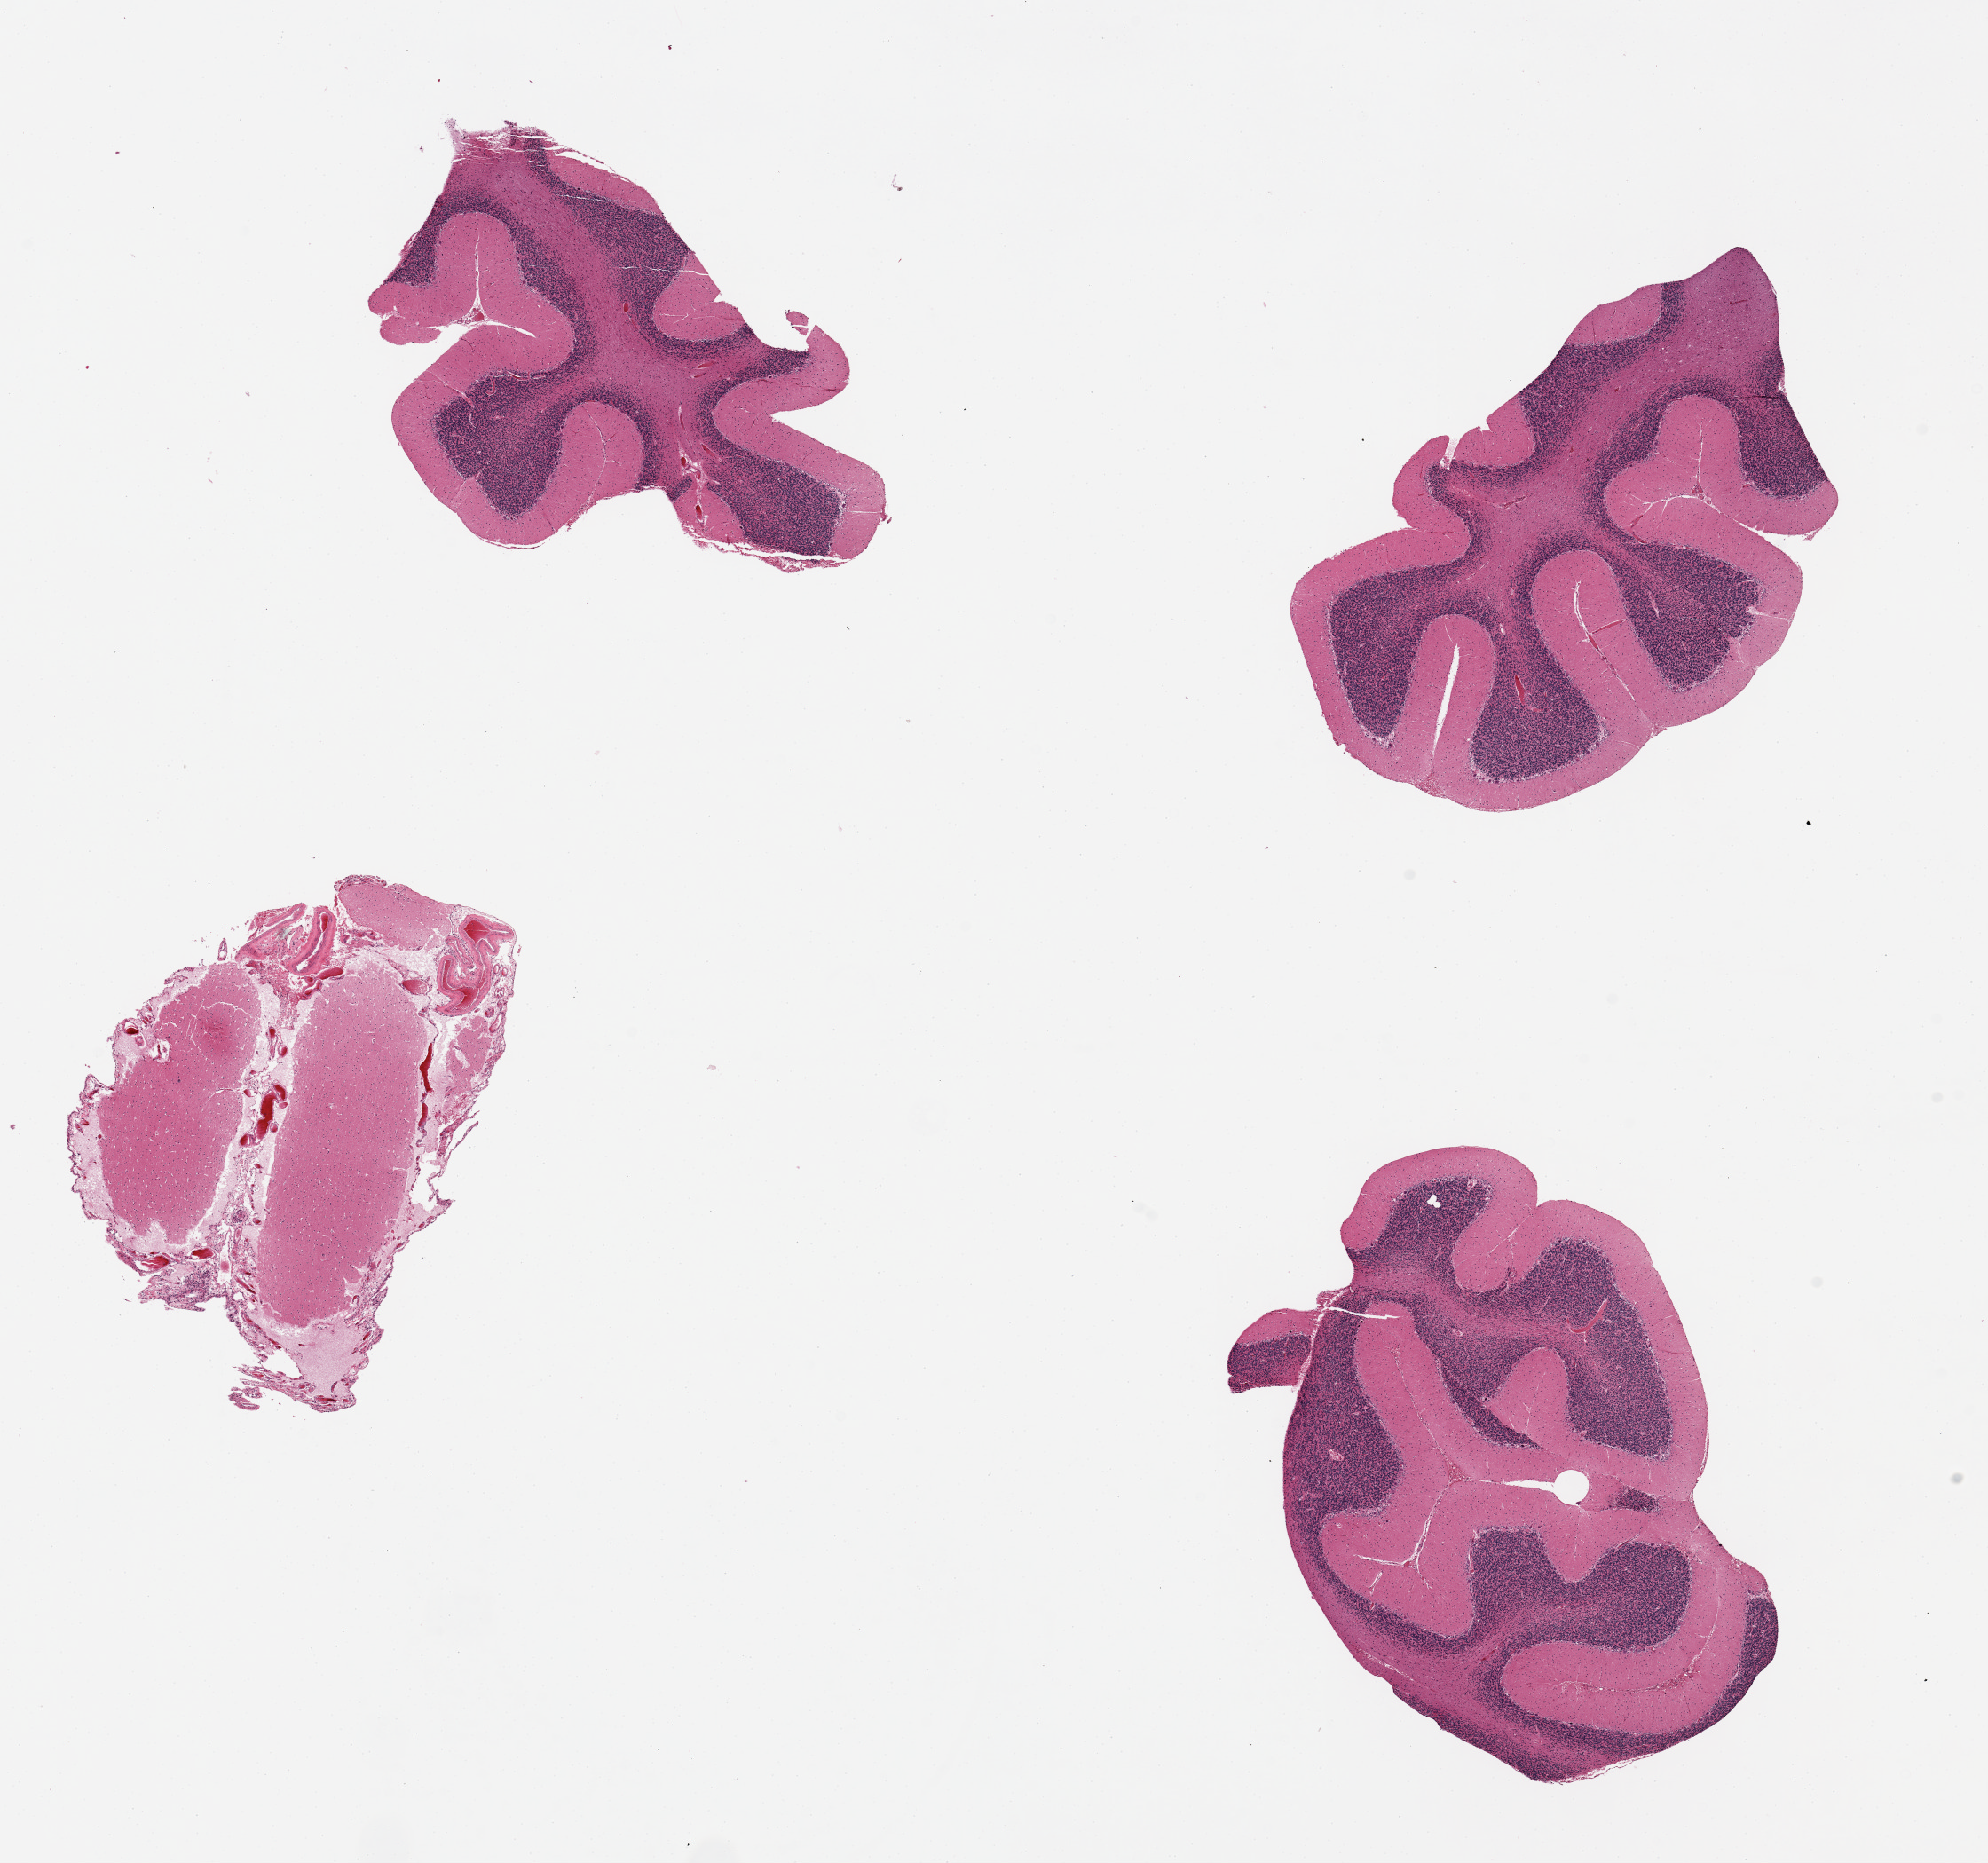
Digitized hematoxylin and eosin (H&E)-stained section, brightfield — shown as a low-resolution overview of the whole scanned area (about 17.7 x 16.6 mm). PAXgene-fixed, paraffin-embedded tissue. Section of cerebellum (target tissue). Tissue donor sample.
Reviewer comment on this tissue sample: 4 pieces, Purkinje layer with minimal hypoxic change.